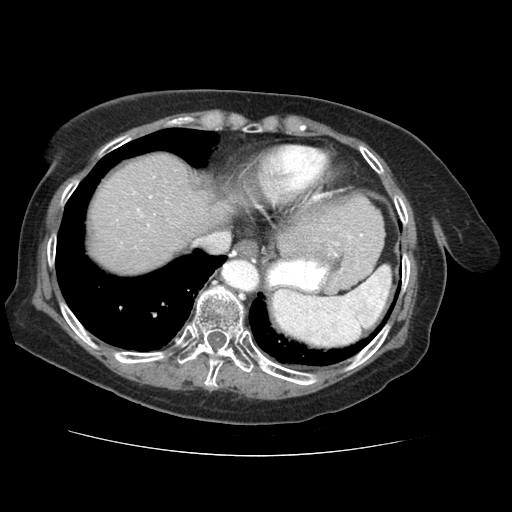
Contrast-enhanced abdominal CT (liver protocol), one axial slice. Slice 56 of 73 in the series (ordered by position). Reconstruction kernel STANDARD. 120 kVp. Soft-tissue window (W 400 / L 40 HU). 512 × 512 image matrix, field of view 360 × 360 mm. From the clinical record (not read from this slice): diagnosis: hepatocellular carcinoma (patient treated with transarterial chemoembolisation; whether this scan precedes or follows treatment is not stated here); TNM stage (as recorded): Stage-IVB; Child-Pugh class: A; tumour nodularity: uninodular.
Structures marked on this image (semi-automatic segmentation, software-assisted and operator-edited):
- liver parenchyma outside the tumour (the mass and vessels are separate outlines, so this box may not span the whole liver): bounding box [x1, y1, x2, y2] px = [90, 154, 230, 272]
- liver vessels: [133, 192, 152, 226]